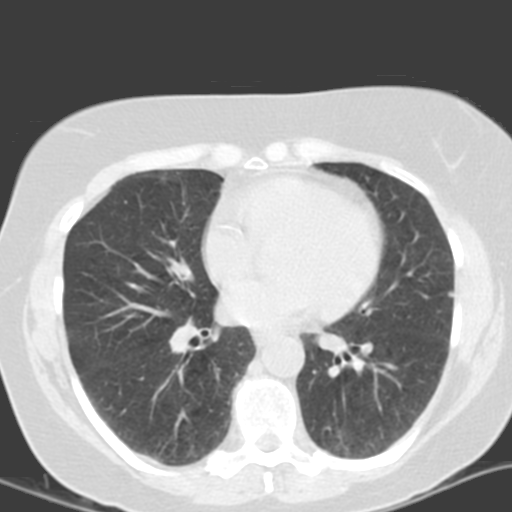
Chest CT (low-dose screening protocol), one axial image. Second screening round (one year after baseline). Lung window (W 1500 / L -600 HU). 3.2 mm slice thickness. Standard (soft-tissue) reconstruction kernel (B). Slice 79 of 161 in the series. 512 × 512 image matrix, field of view 290 × 290 mm. Female participant, aged 55 years at enrolment.
Expert reader's lesion annotation, box from (x=304, y=411) to (x=377, y=465) px. The screening reader recorded 4 non-calcified nodules or masses ≥4 mm on this exam (left lower lobe, left lower lobe, left upper lobe, right middle lobe); which of them this box marks is not recorded. Later outcome: lung cancer diagnosed 688 days after this screen — adenocarcinoma with mixed subtypes, left lower lobe, poorly differentiated (G3), stage IA (AJCC 6th edition), 21 mm at pathology.